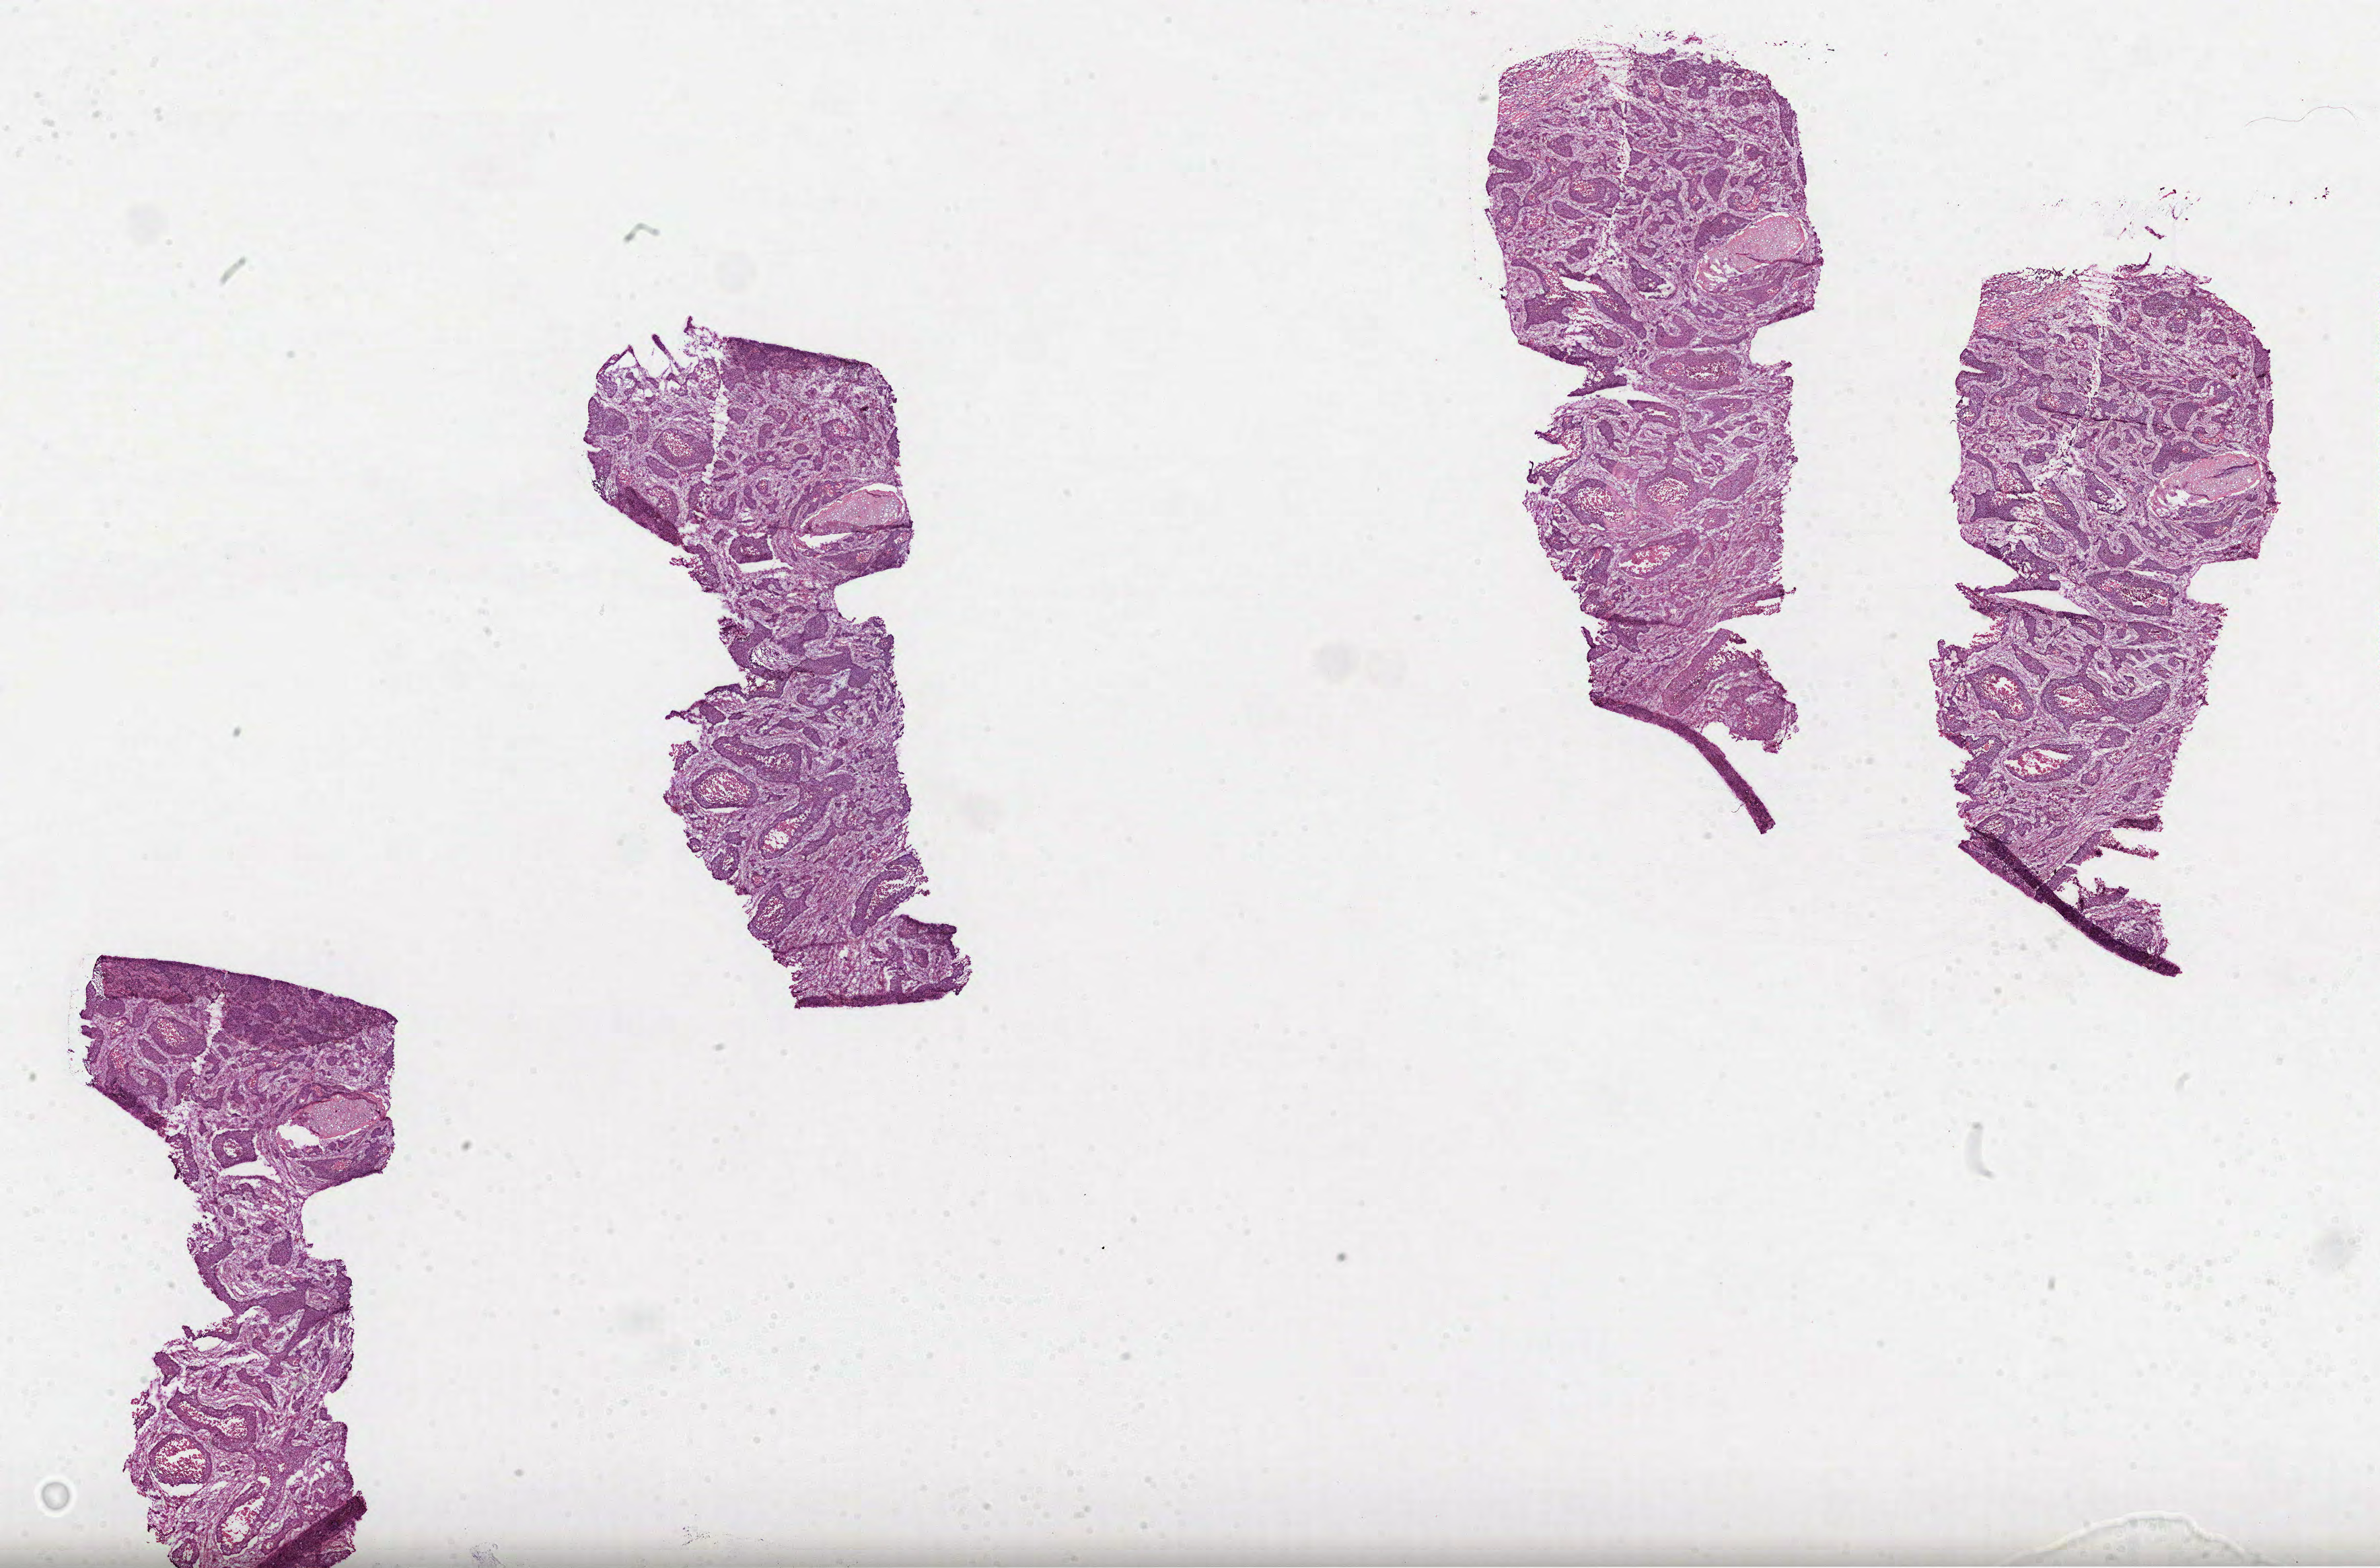
Digitized H&E-stained tissue section (whole slide), low-resolution overview of the scanned area, about 28.5 x 18.8 mm, formalin-fixed paraffin-embedded (FFPE) diagnostic section, primary tumour sample from the lung. Patient: male, age at initial diagnosis 55 years.
Histologic diagnosis: Squamous cell carcinoma, NOS (upper lobe, lung). AJCC pathologic stage: IIB. Laterality: right.